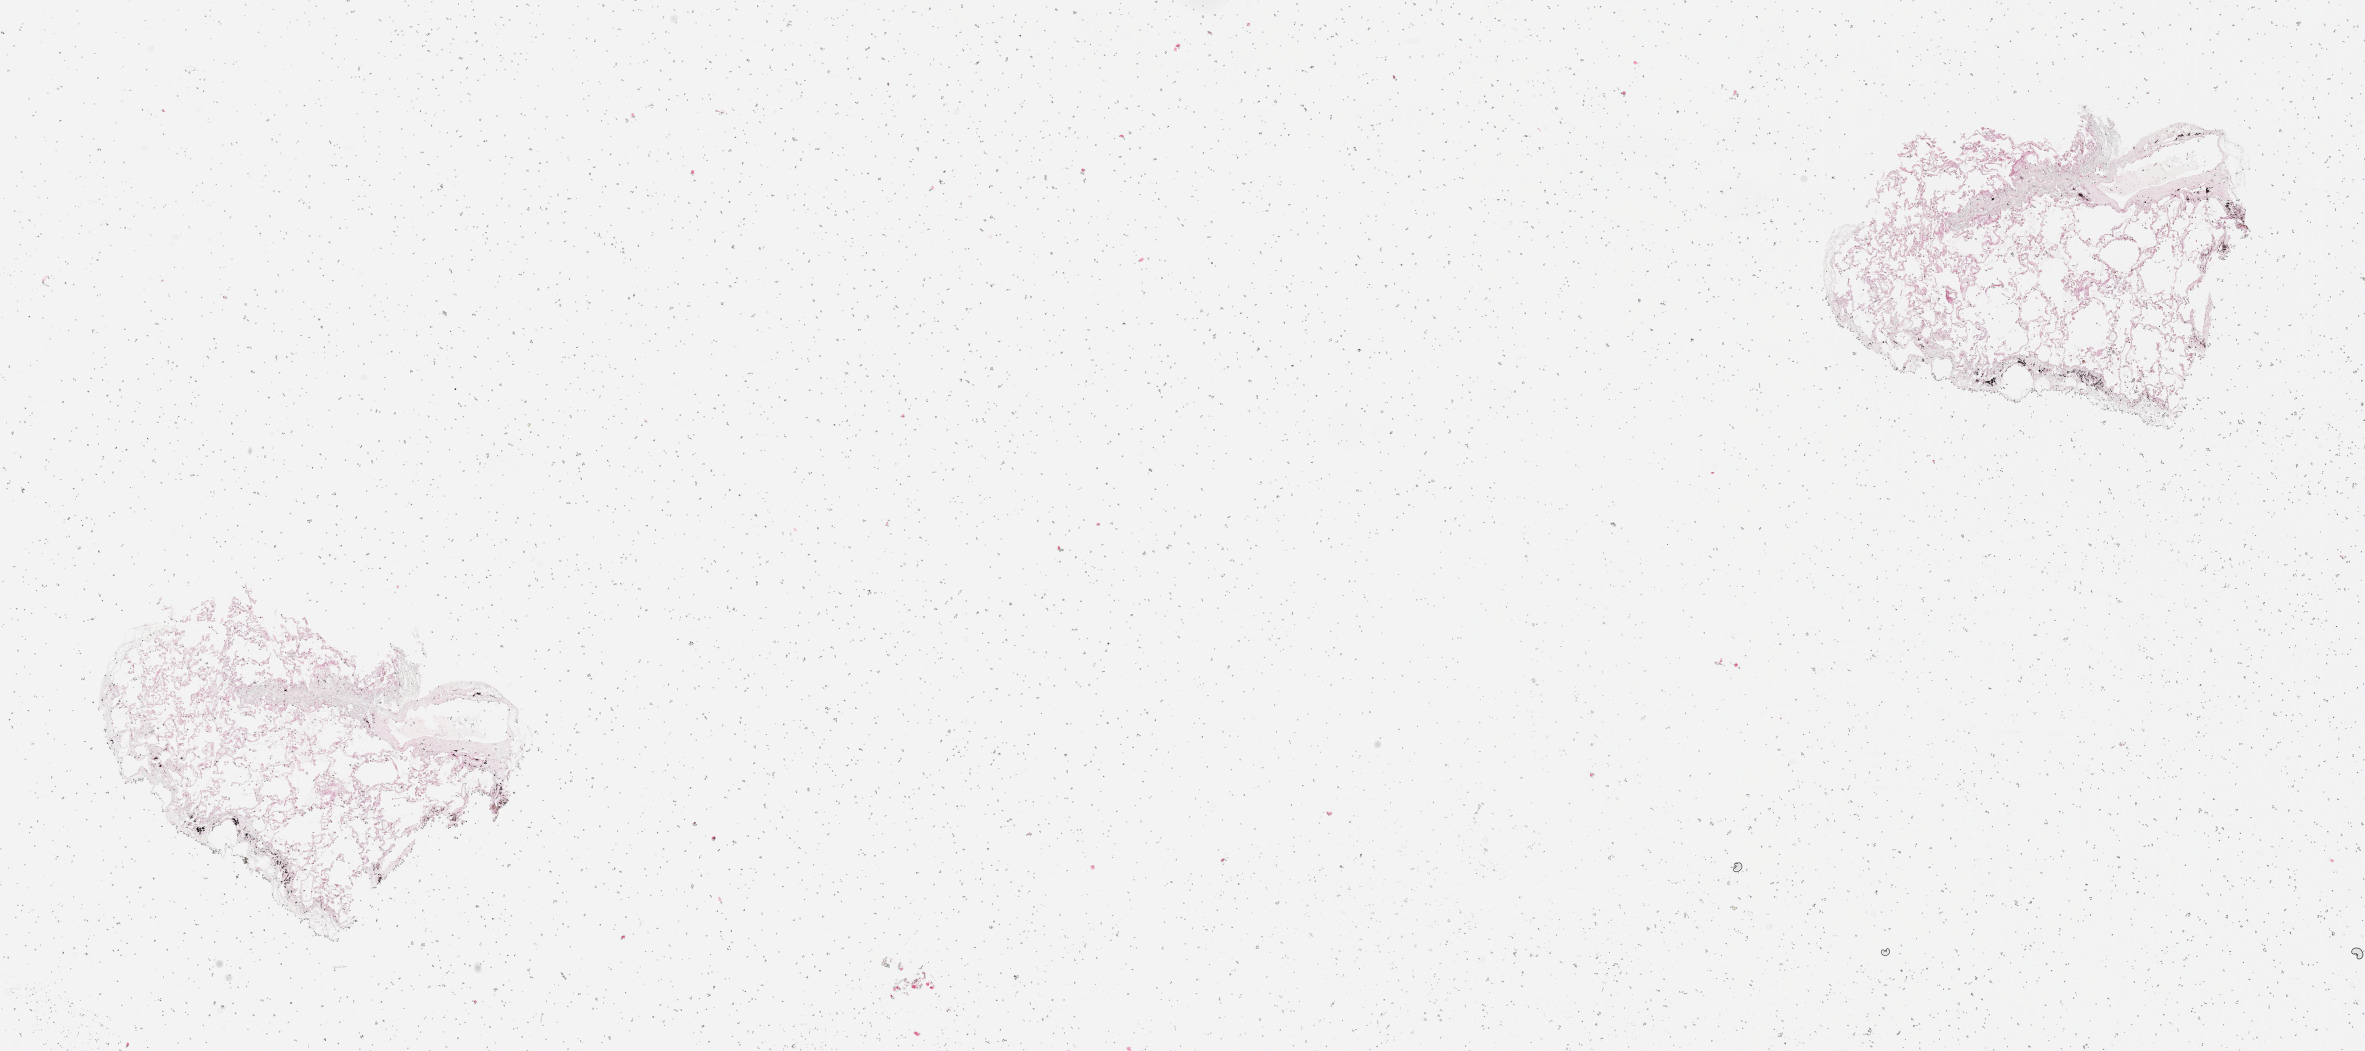
H&E whole-slide image, whole scanned area (about 19.0 x 8.5 mm, slide scanned at 20x) shown as a low-resolution overview, lung, tissue type not recorded.
Patient diagnosis (cohort enrolment): squamous cell carcinoma (lung).